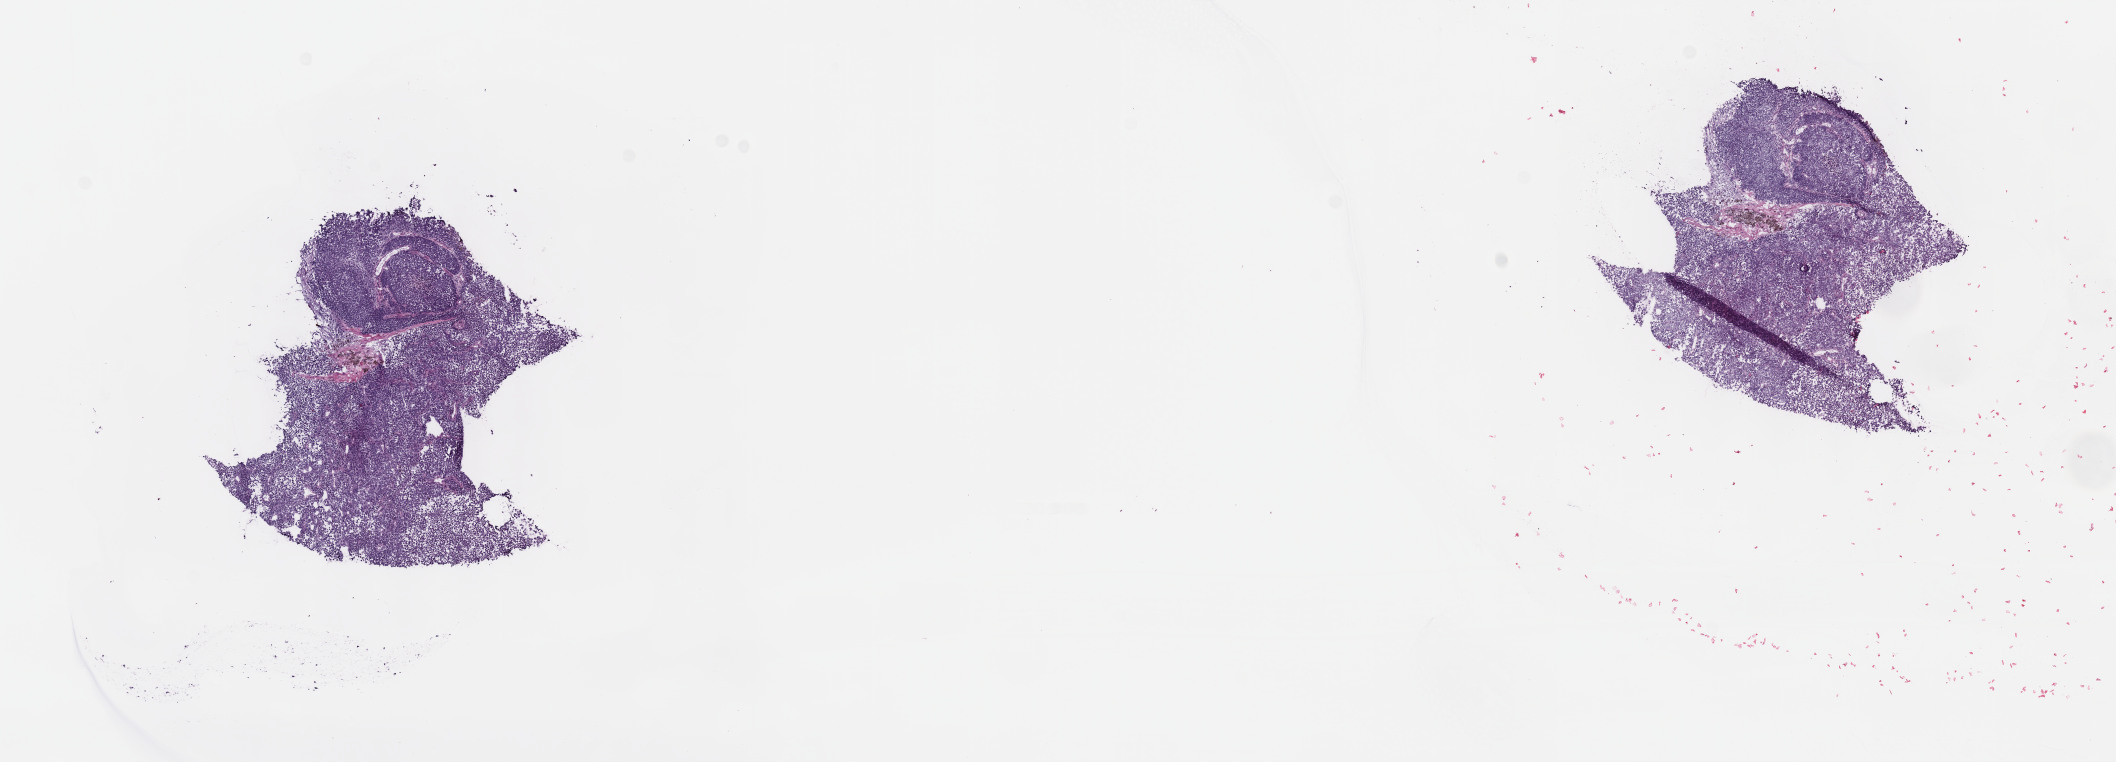
H&E-stained whole-slide image, whole scanned area (about 17.1 x 6.2 mm, acquisition: 40x scan) shown as a low-resolution overview, frozen section from the top of the tissue portion, primary tumour sample from the uvea. Patient: male, age at initial diagnosis 53 years. Pathologist review of this section (percent, as recorded): tumour cells 100%, tumour nuclei 80%, normal cells 0%, stromal cells 0%, necrosis 0%. Infiltration values recorded for this section: lymphocyte infiltration 1%, monocyte infiltration 0%, neutrophil infiltration 0%.
• AJCC pathologic stage: IIB (7th edition)
• laterality: left
• histologic diagnosis: Mixed epithelioid and spindle cell melanoma (choroid)